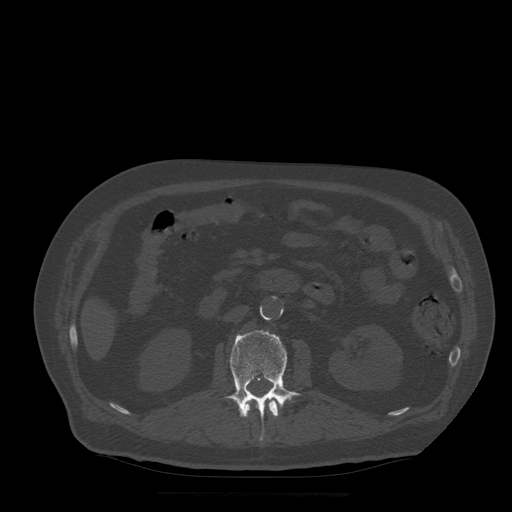
CT including the spine, one axial slice. Slice 170 of 522 in the series (ordered by position). Bone window (W 1800 / L 400 HU). 512 × 512 image matrix. Patient age 72 years. Case-level facts recorded for this patient, not image findings: primary cancer: prostate.
Outlined on this slice (semi-automatically segmented with operator editing):
- L1 vertebra: box from (x=244, y=397) to (x=279, y=417) px
- L2 vertebra: (x=225, y=331)–(x=301, y=441)